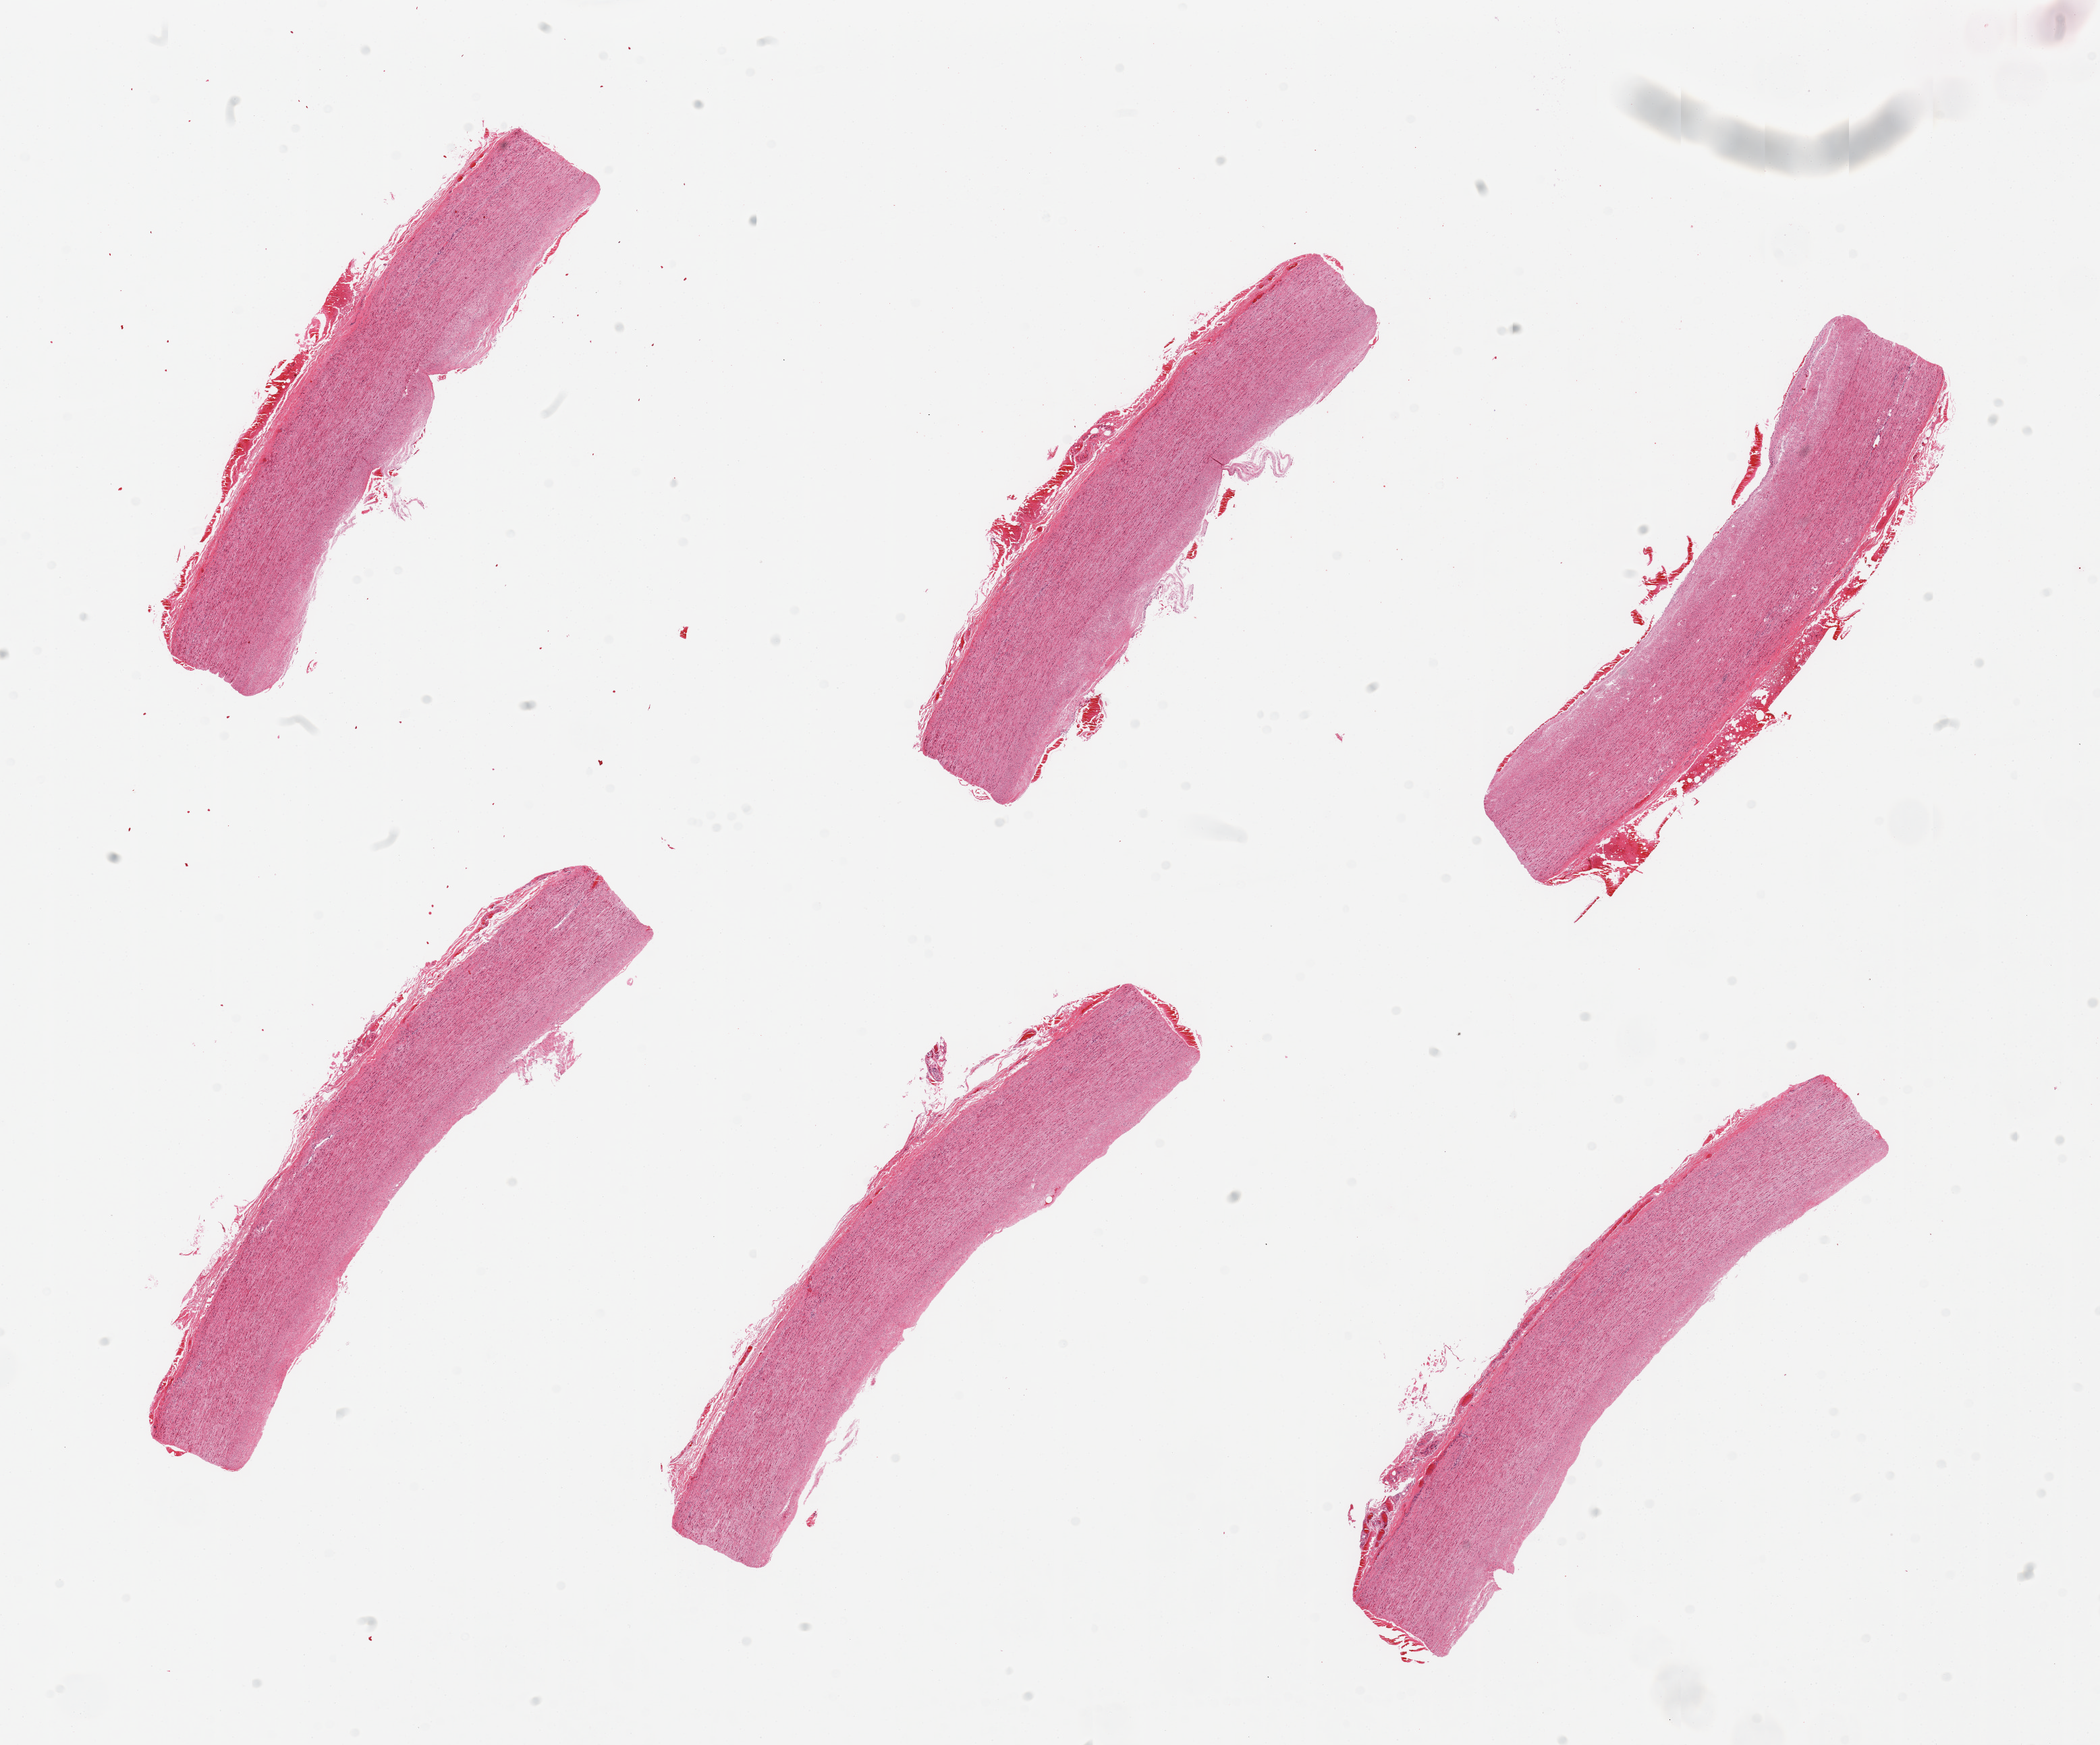
Whole-slide image, haematoxylin and eosin stain, brightfield — whole scanned area (about 24.6 x 20.5 mm) shown as a low-resolution overview. PAXgene-fixed, paraffin-embedded tissue. Target tissue: aorta. Donor tissue sample. Donor sex: male.
- review note (as recorded): 6 pieces, trace ahdherent serosa